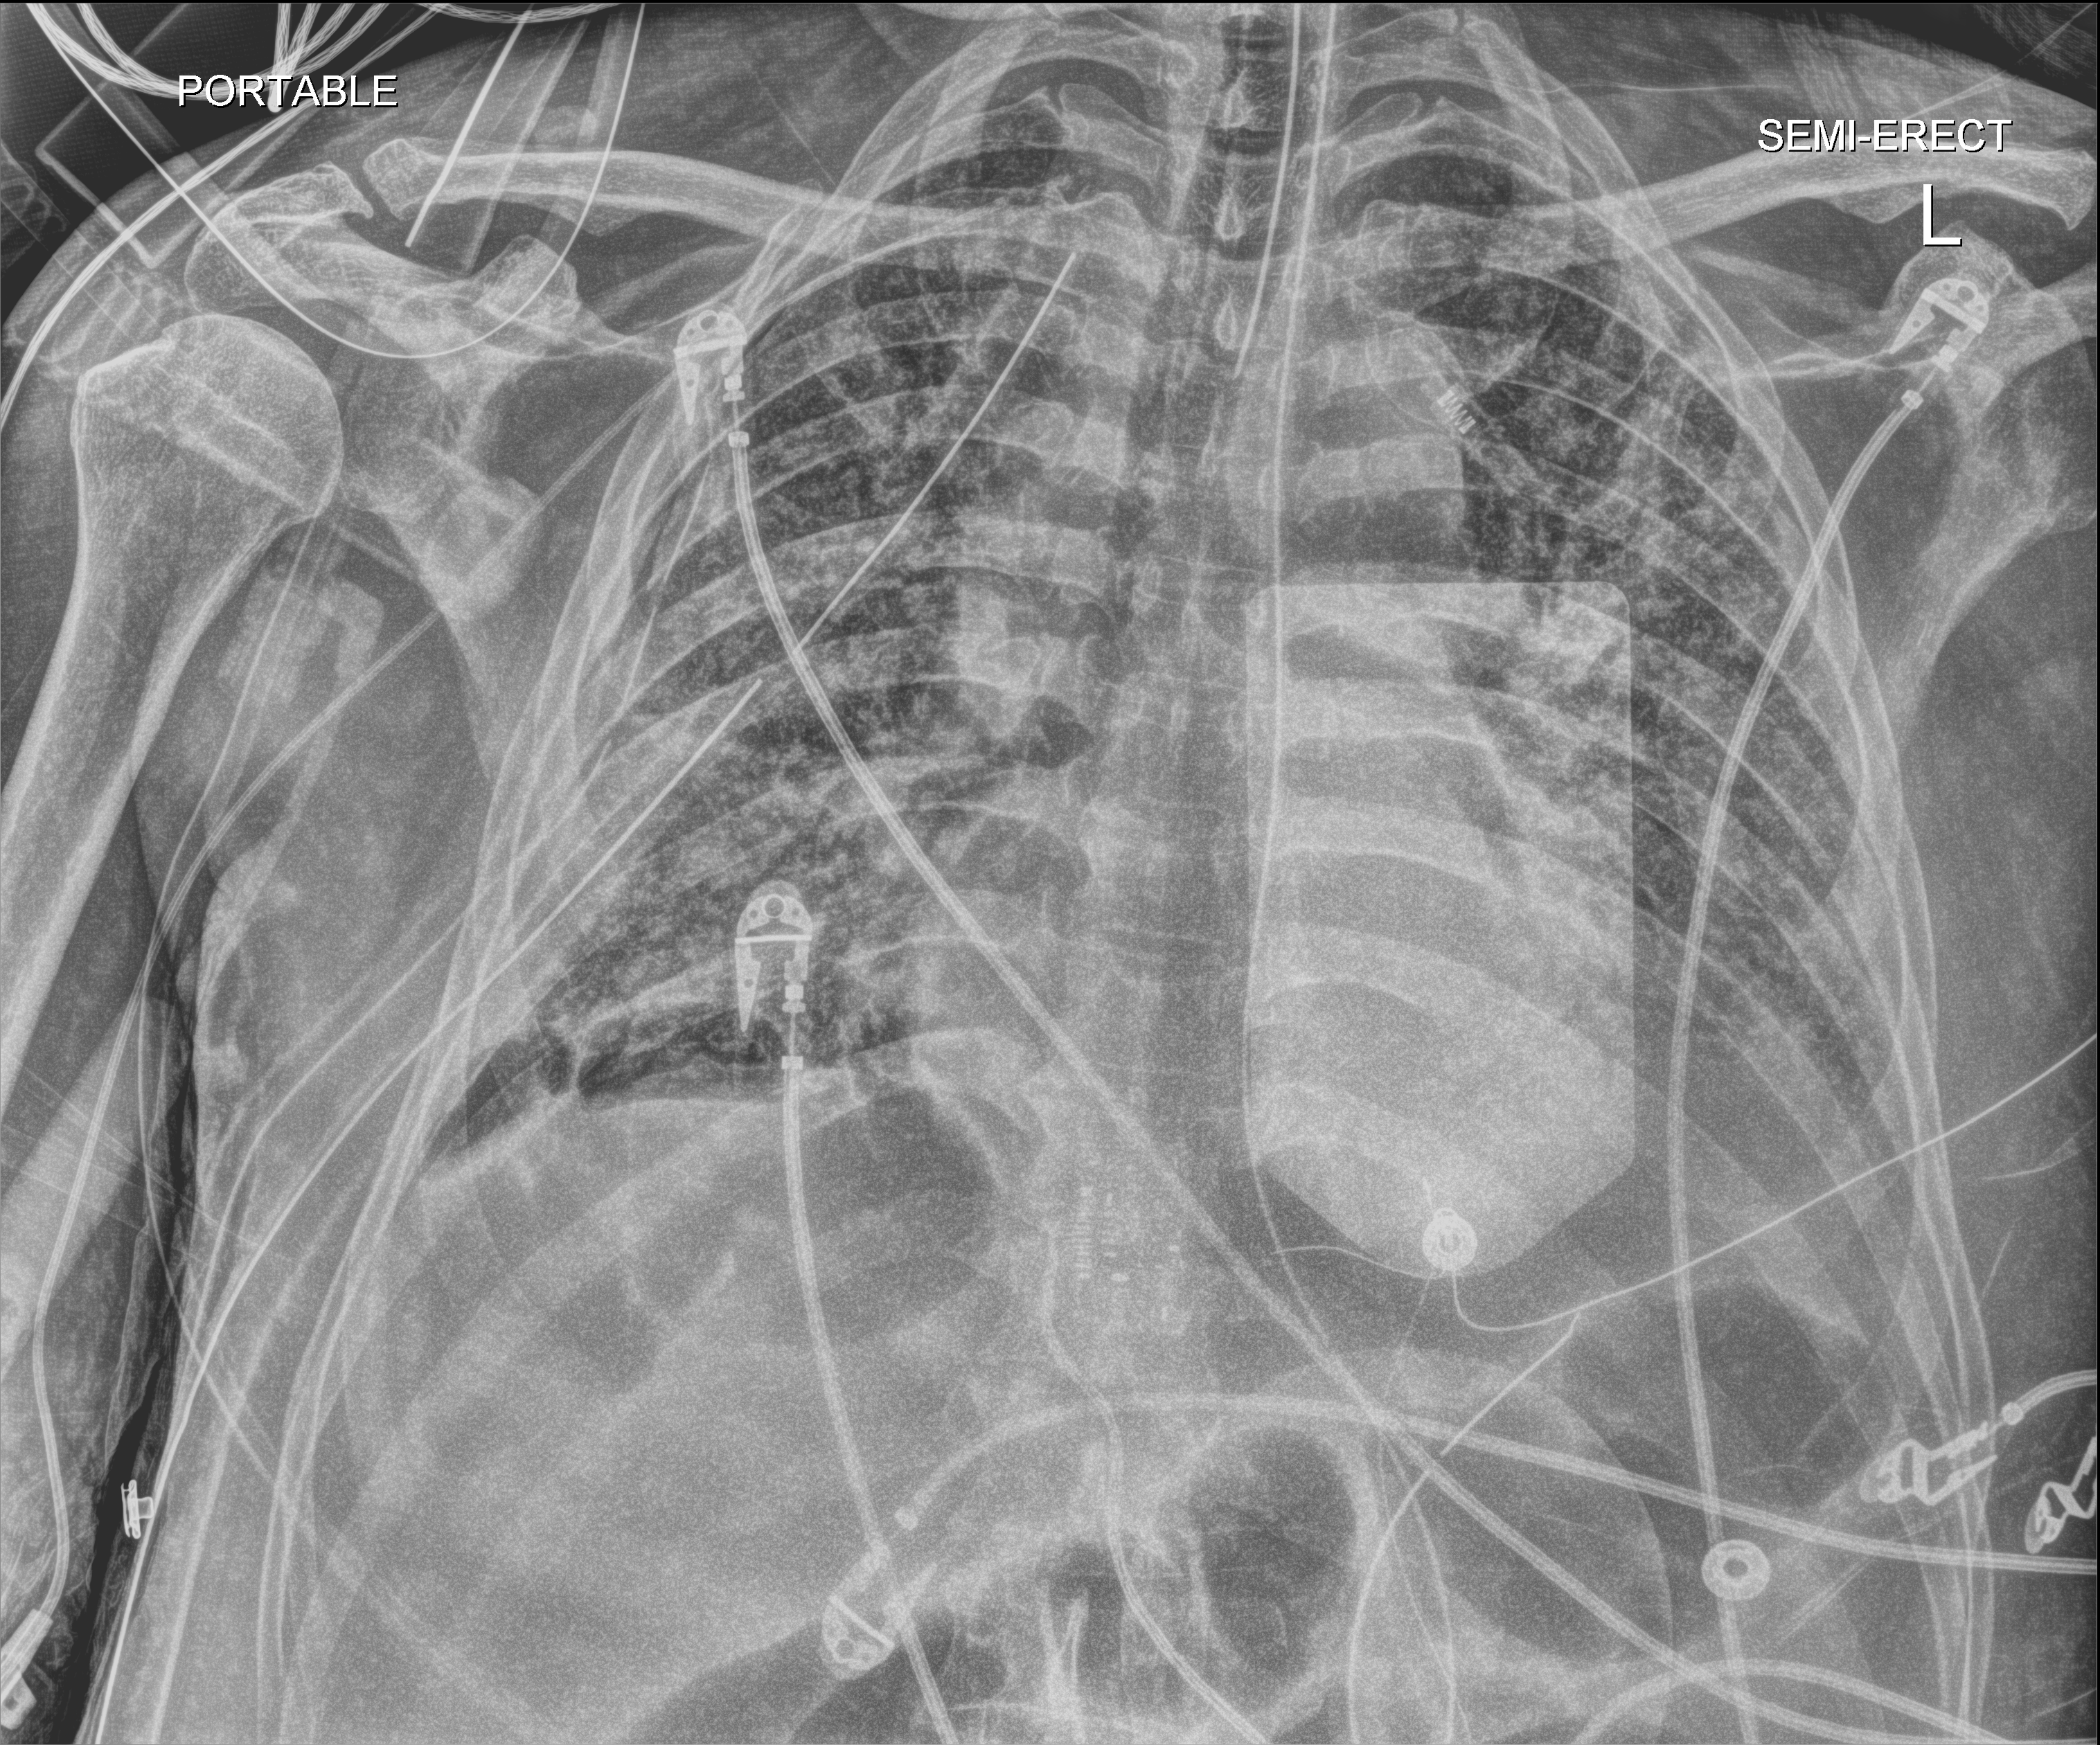
Chest X-ray. Patient hospitalised with COVID-19; male, aged 60–74 years.
Hospital-stay facts (about this admission, not read from this image; timing relative to this image not recorded): length of hospital stay: 37 days; admitted to intensive care during this hospital stay: yes.